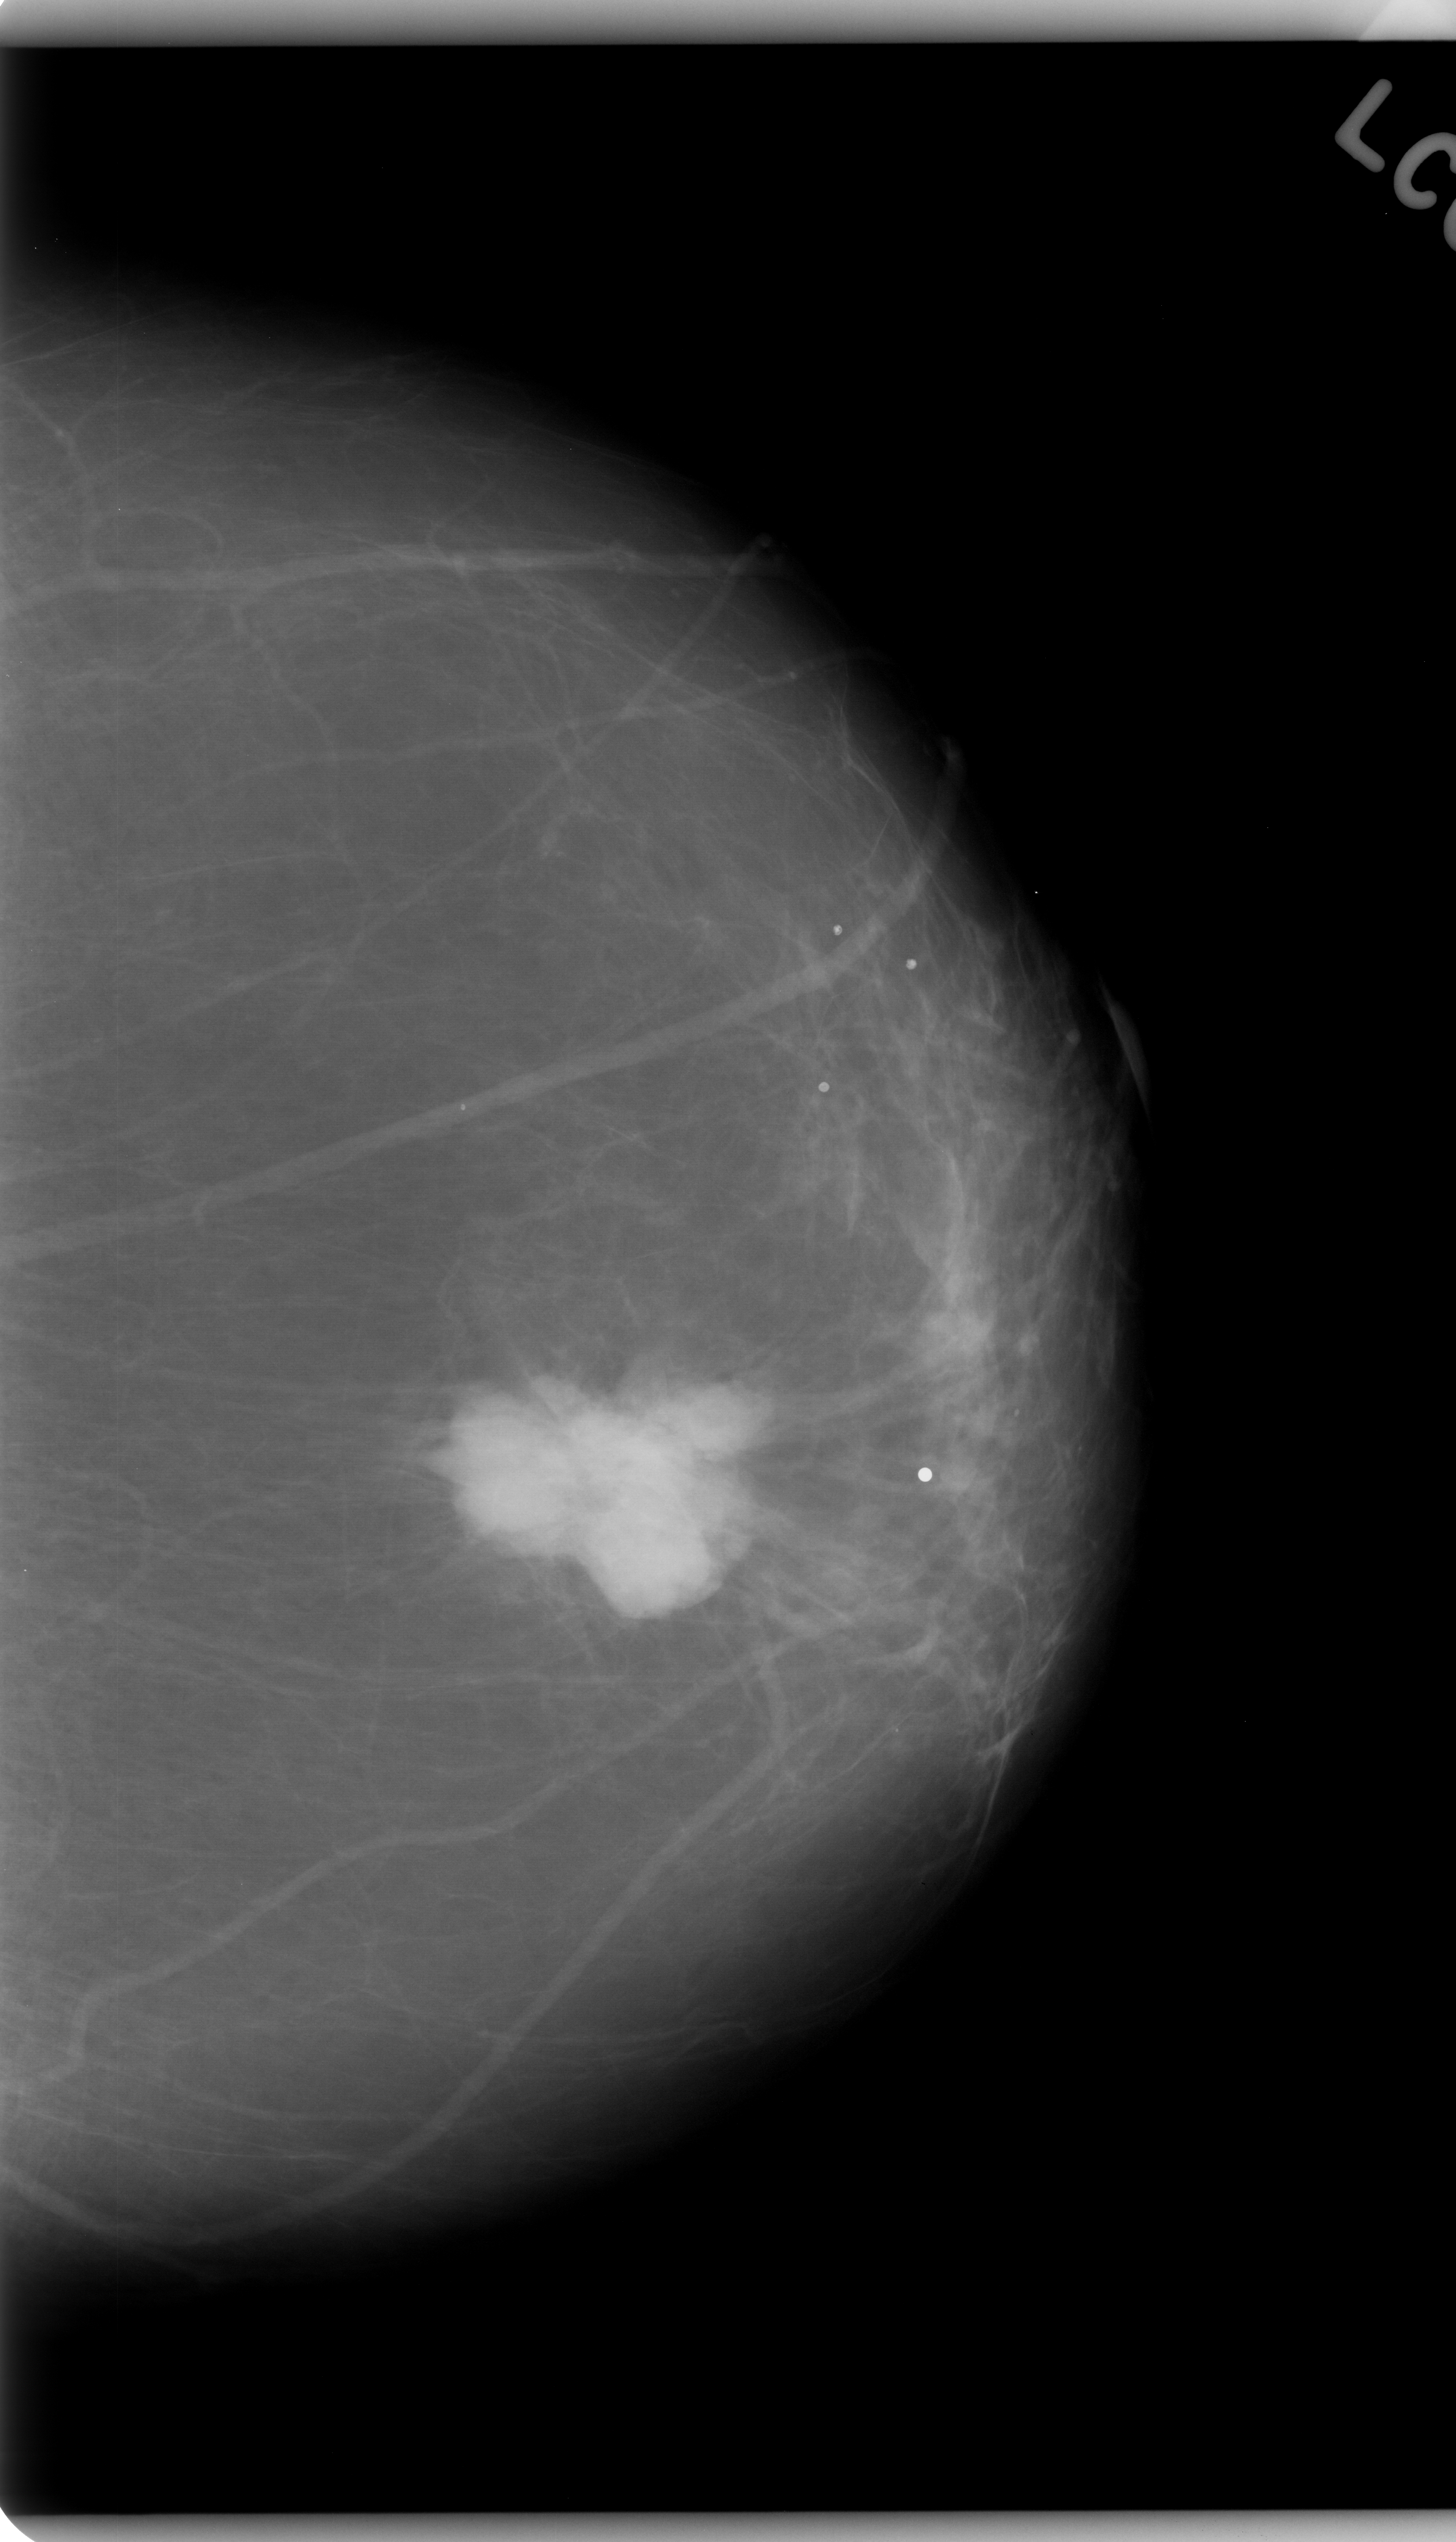
Digitized screen-film mammogram, left breast, craniocaudal (CC) view, breast composition: almost entirely fatty (BI-RADS density category 1 of 4).
Marked findings (only marked abnormalities are described; nothing is implied about the rest of the image): mass, shape lobulated, margins microlobulated; BI-RADS assessment category 5; pathology result (as recorded, not read from the image): malignant.